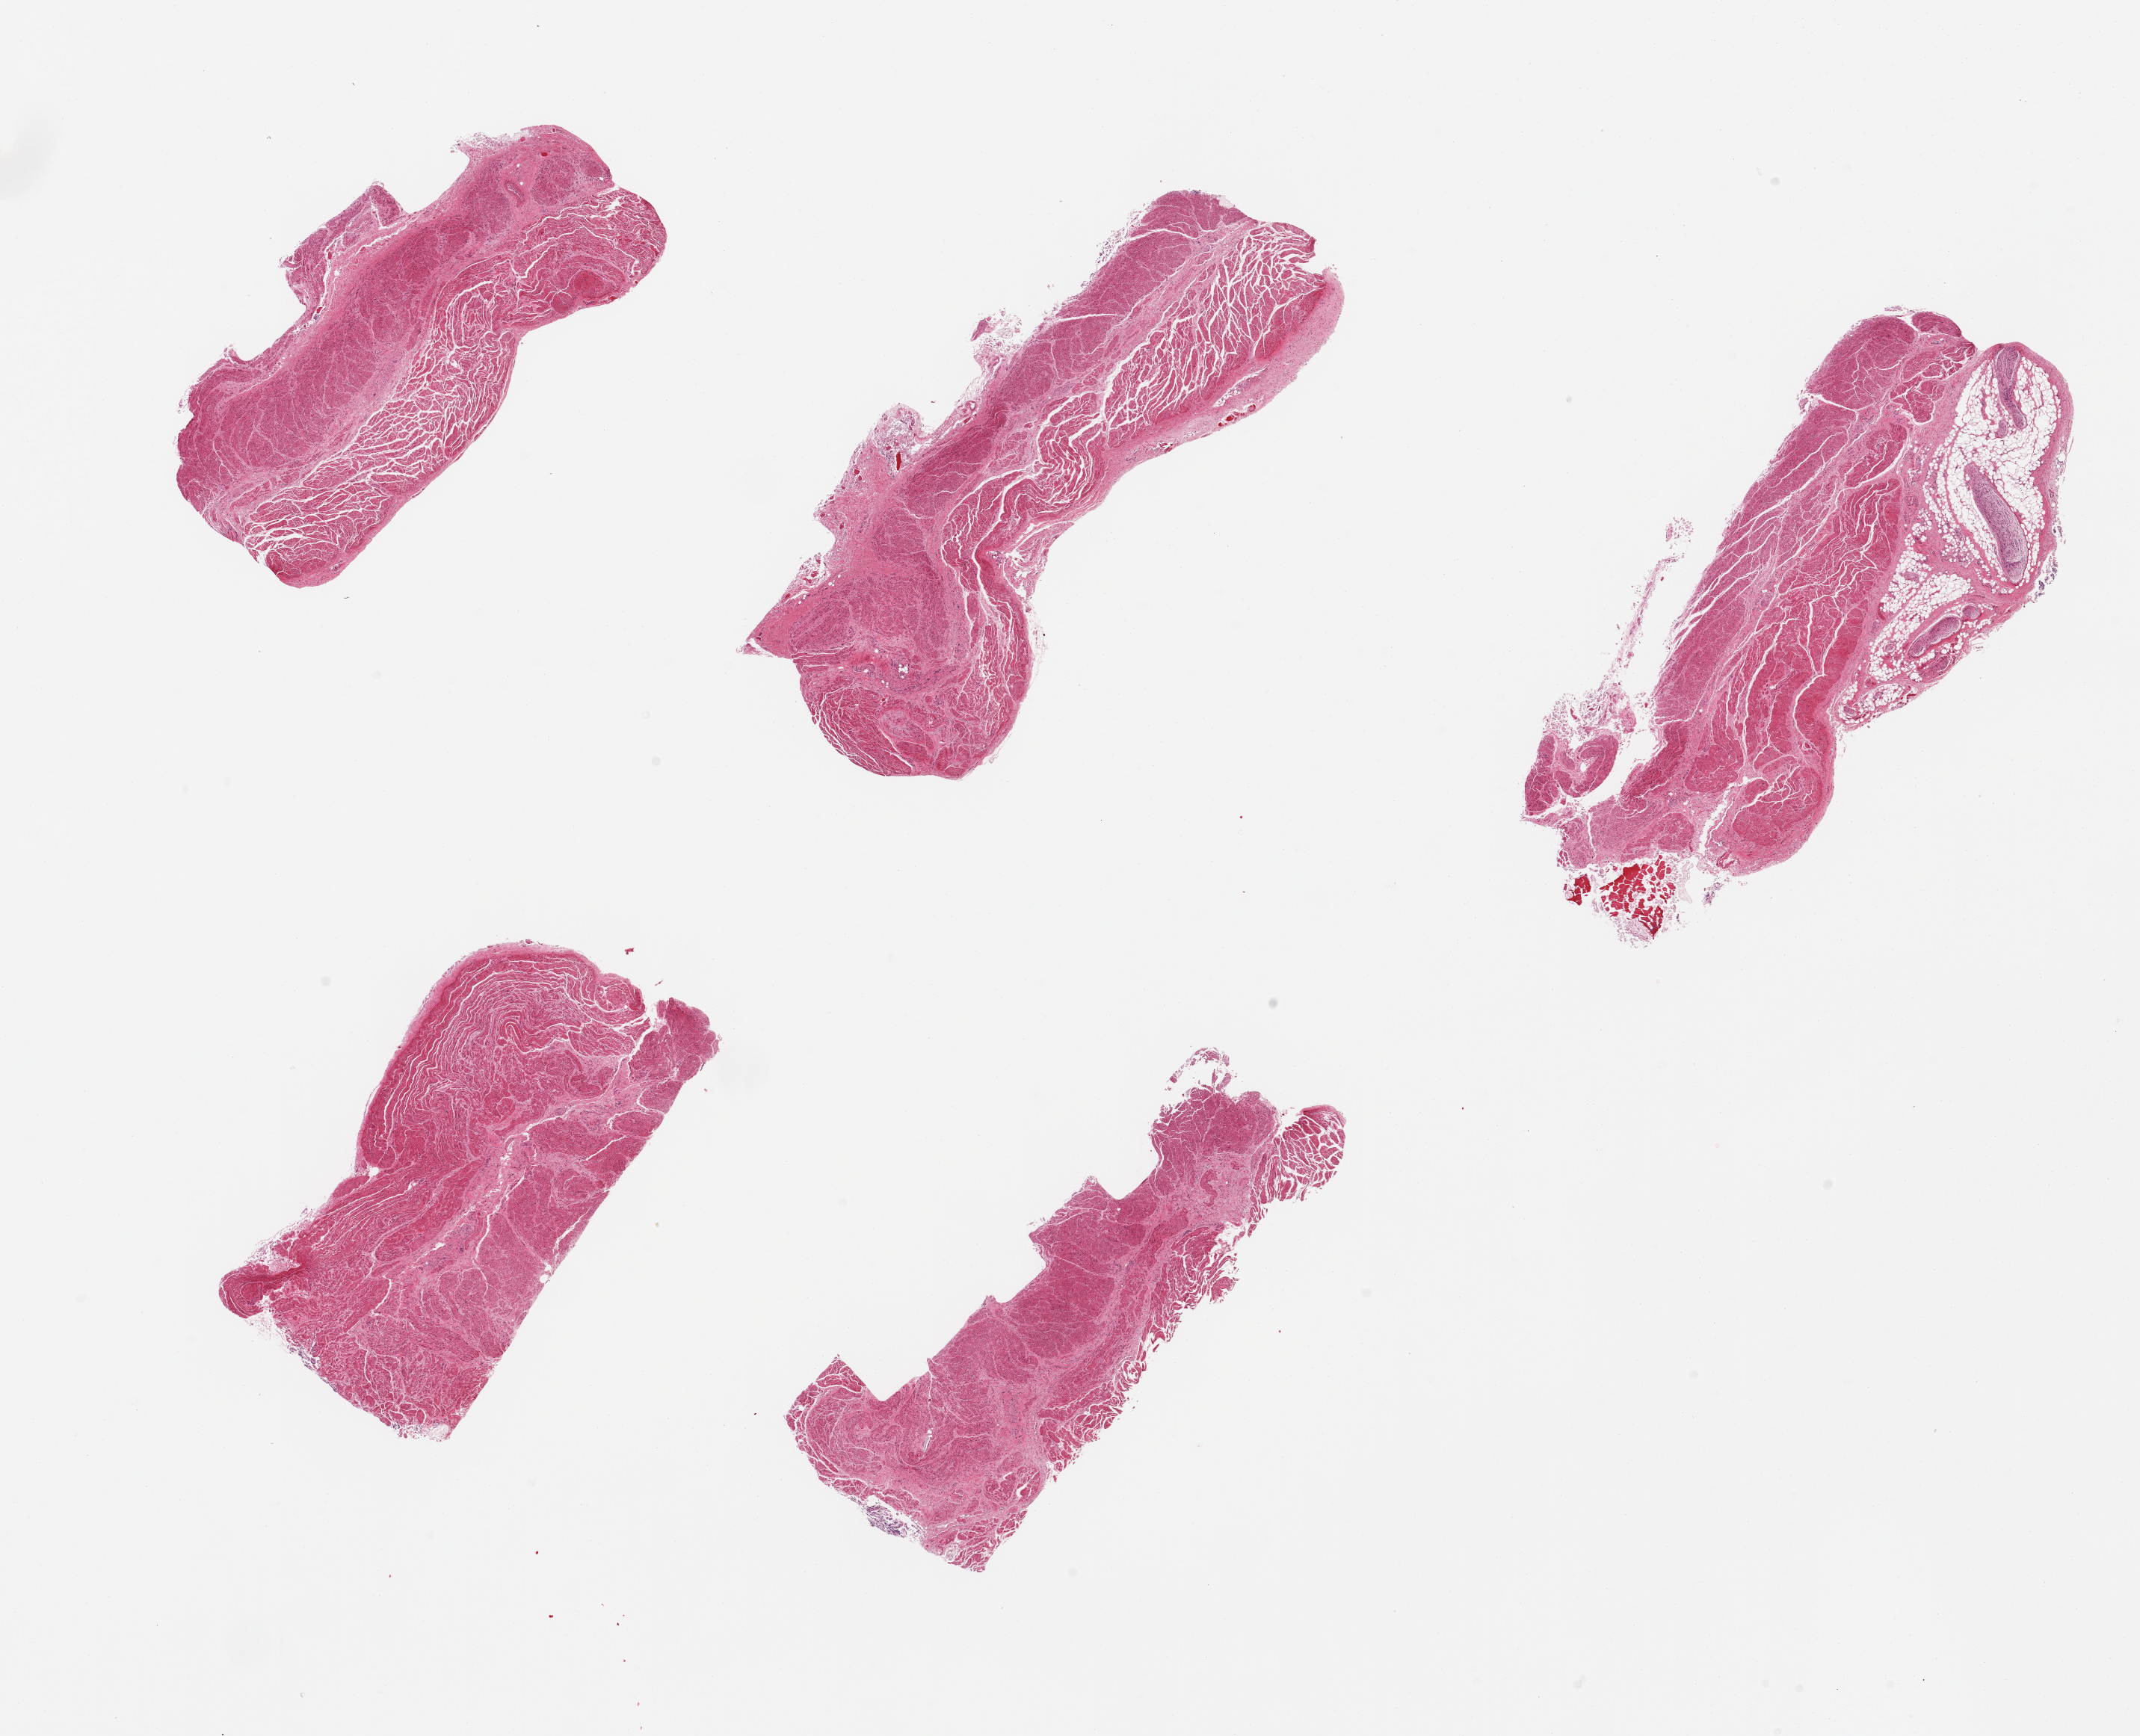
Digitized hematoxylin and eosin (H&E)-stained section, brightfield, a low-resolution overview of the entire scanned area, about 22.6 x 18.4 mm (from a 20x scan); PAXgene-fixed paraffin-embedded (PFPE) section; sampled site (target tissue): gastroesophageal junction; tissue donor sample. Donor: male.
Reviewer comment on this tissue sample: 5 pieces, target muscularis, adherent nubbin of serosal fat up to ~1mm.